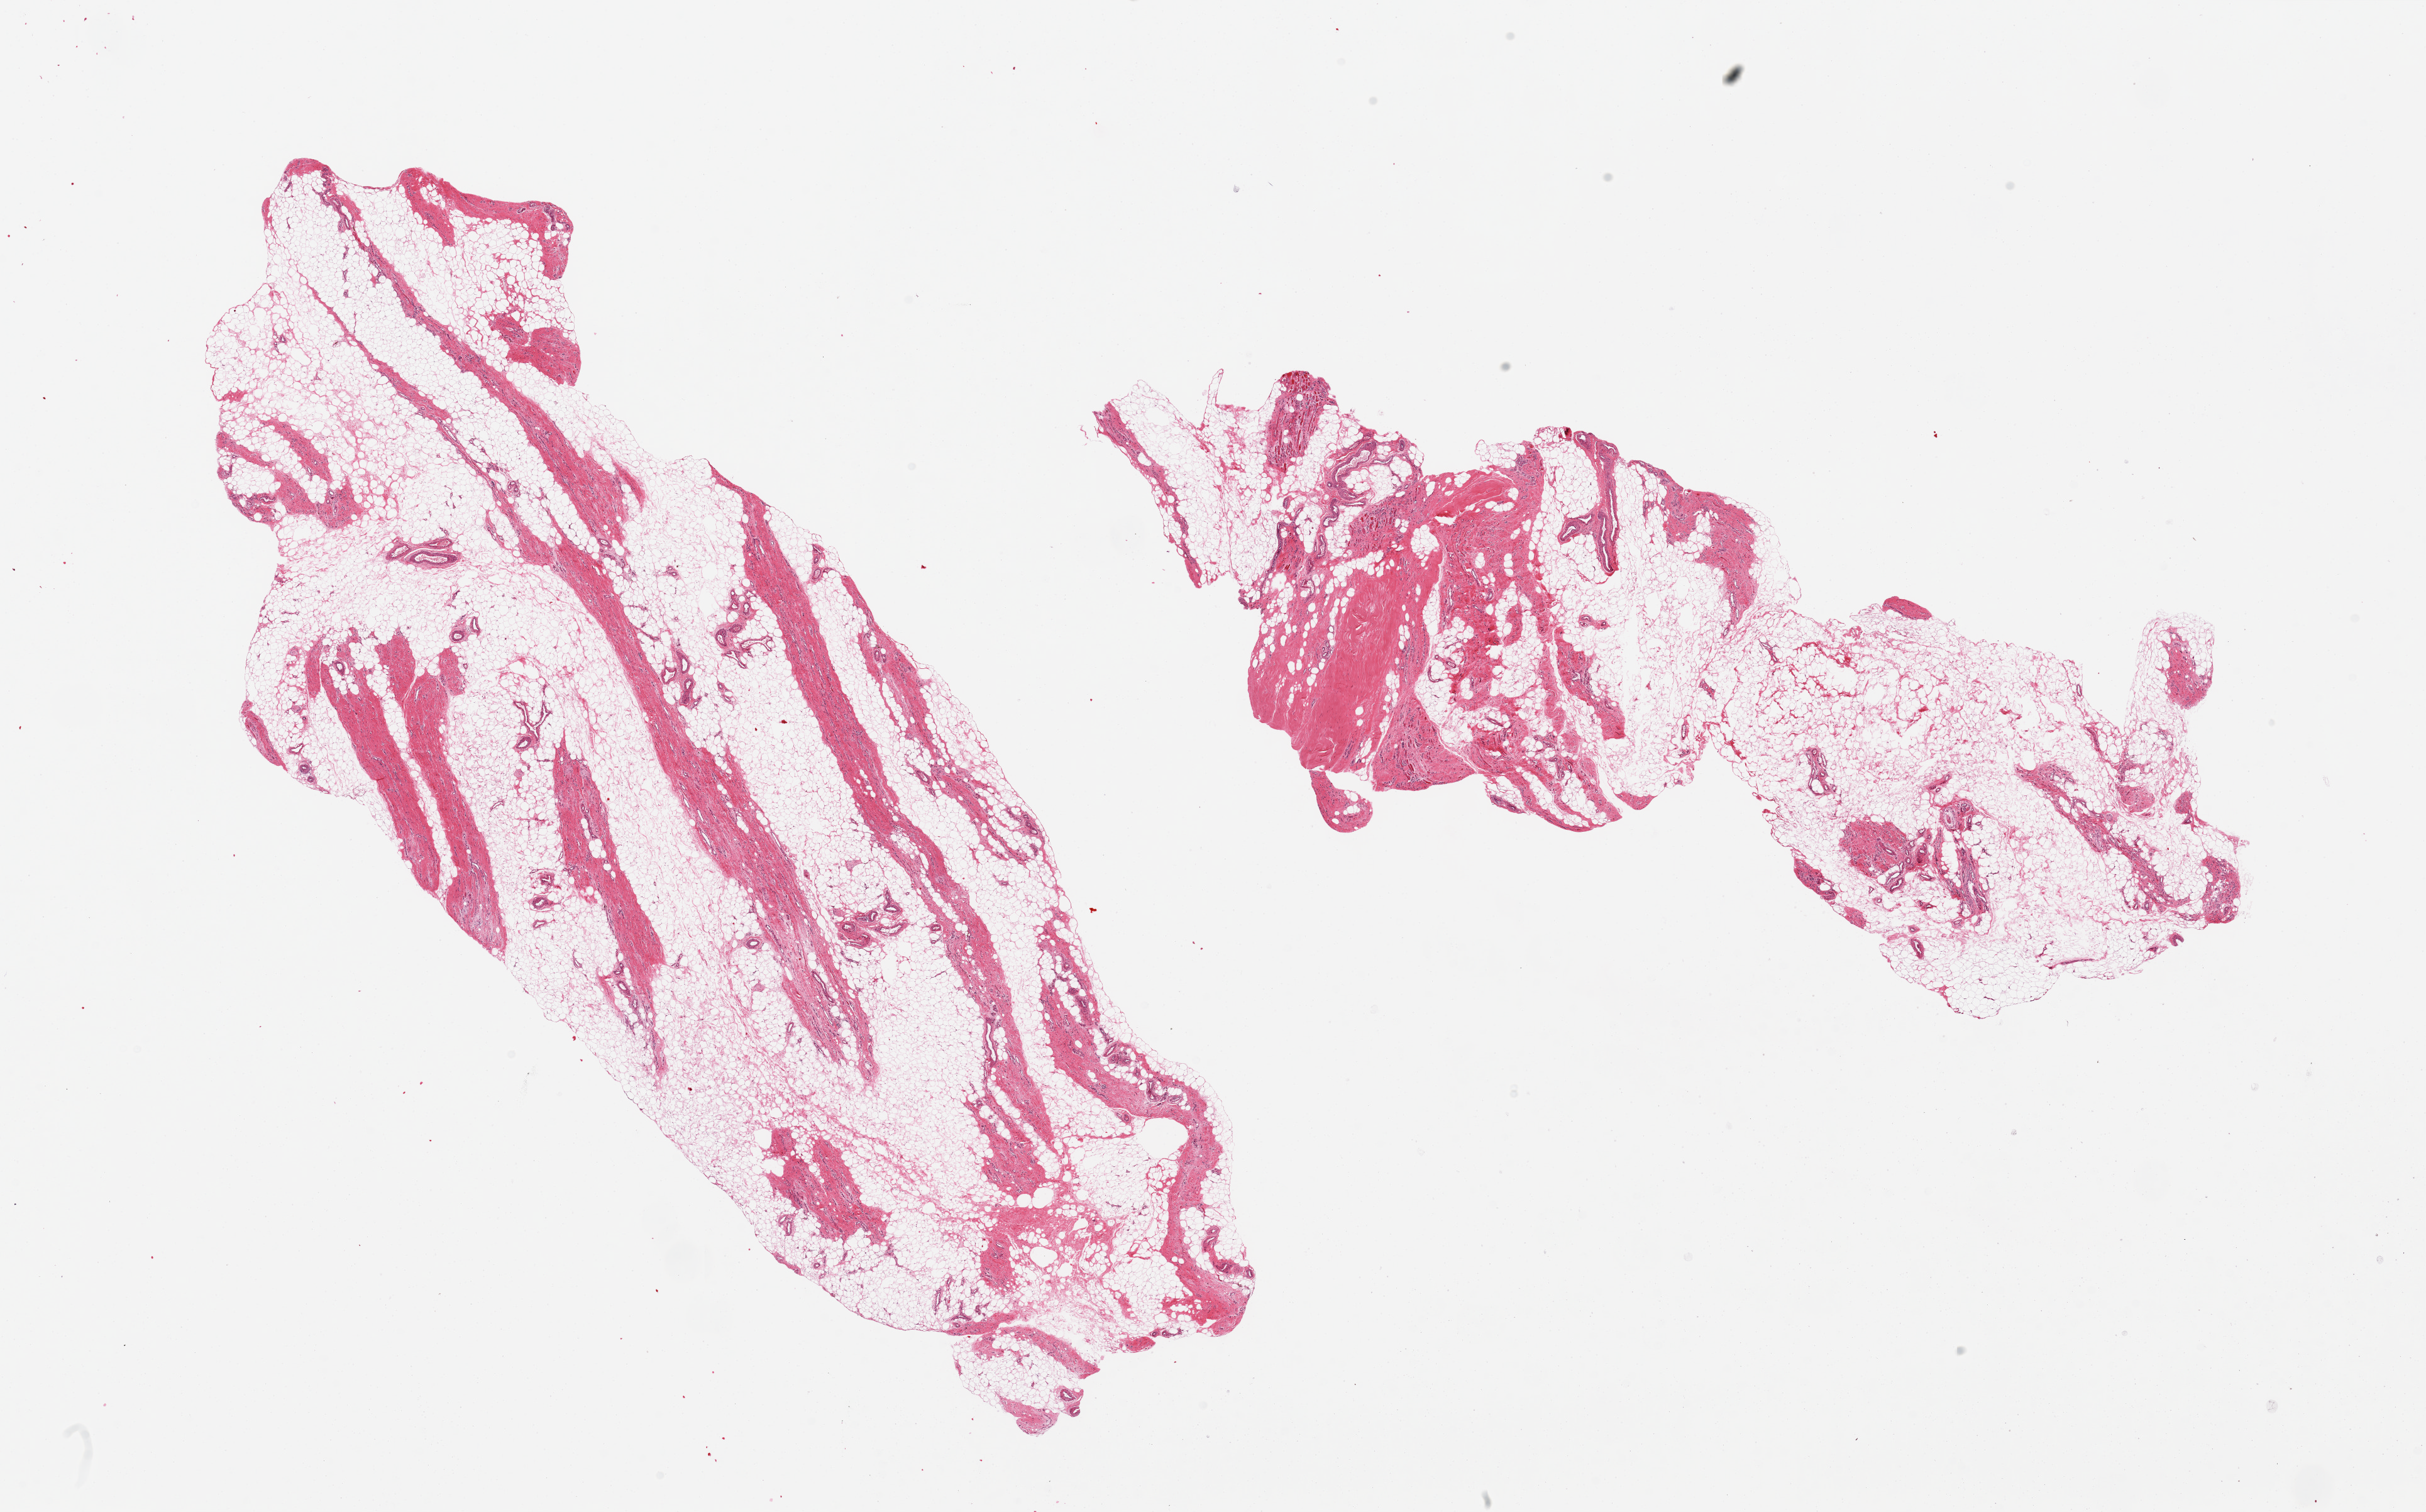
Hematoxylin and eosin (H&E) whole-slide image, brightfield — whole scanned area (about 30.5 x 19.0 mm, slide scanned at 20x) shown as a low-resolution overview; PAXgene-fixed paraffin-embedded (PFPE) section; target tissue: skeletal muscle; donor tissue sample. Donor sex: male.
Pathologist's review note for this sample: 2 pieces mainly fat with fibroadipose tissue, only trace skeletal muscle.